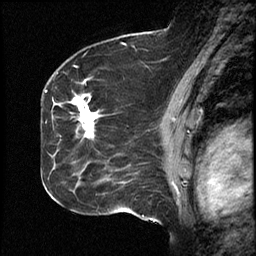
Breast MRI (dynamic contrast-enhanced), one sagittal slice. Slice 29 of 46 in the series (ordered by position). Dynamic contrast-enhanced study with each time point stored as its own series, time point 2 of 4 at this slice position (early post-contrast, ordered by acquisition time). 1.5 T. TE 4.2 ms, TR 18.3 ms. 256 × 256 image matrix. Case-level facts recorded for this patient, not image findings: setting: breast cancer imaged before/during neoadjuvant chemotherapy; receptor status: HR-positive, HER2-negative.
Structures marked on this image (semi-automatic segmentation, software-assisted and operator-edited):
- analysis volume of interest (the breast-tissue region the enhancement analysis was run in; not a lesion): bounding box (x1, y1, x2, y2) in pixels: (64, 74, 111, 196)
- tumour enhancement mask (voxels above the 100 % enhancement threshold inside the analysis volume of interest): (78, 97, 96, 135)